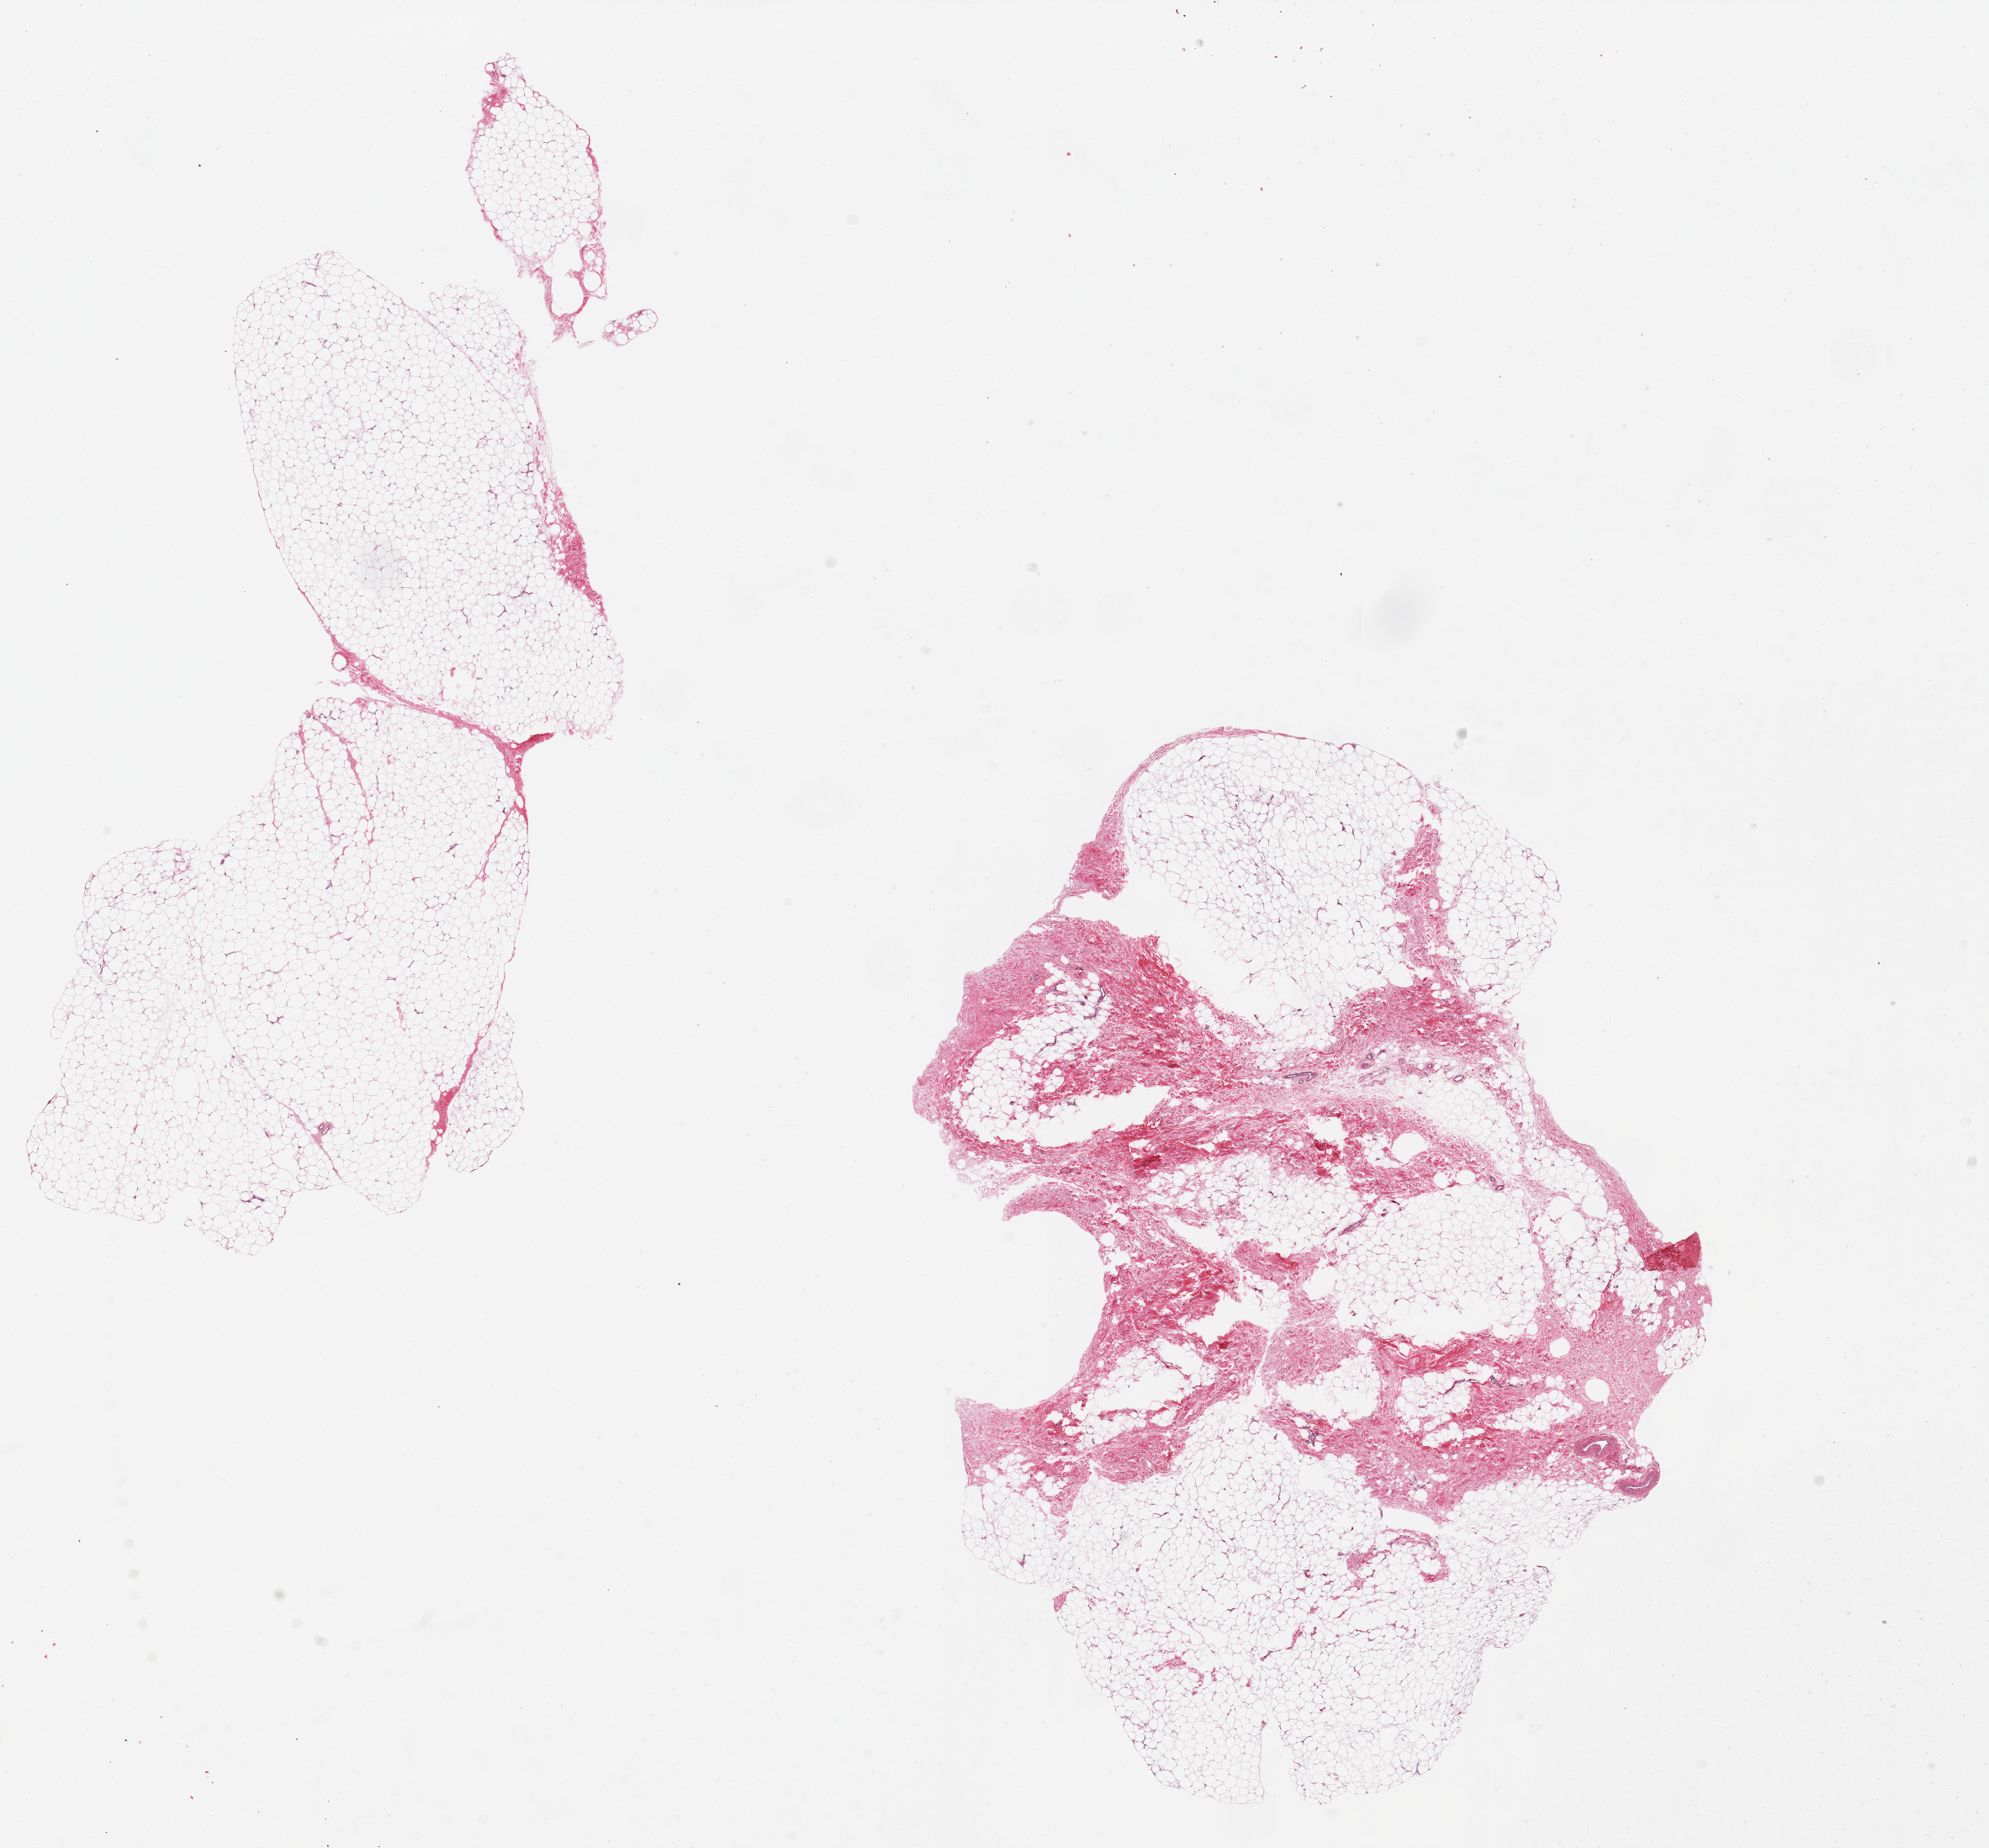
H&E whole-slide image, whole scanned area (about 18.7 x 17.4 mm) shown as a low-resolution overview, PAXgene-fixed, paraffin-embedded tissue, section of breast (target tissue), tissue donor sample. Donor sex: male.
Review note (as recorded): 2 pieces. 12x4 & 10x6mm; 1 fibroadipose, no ducts; 1 adipose no ducts.